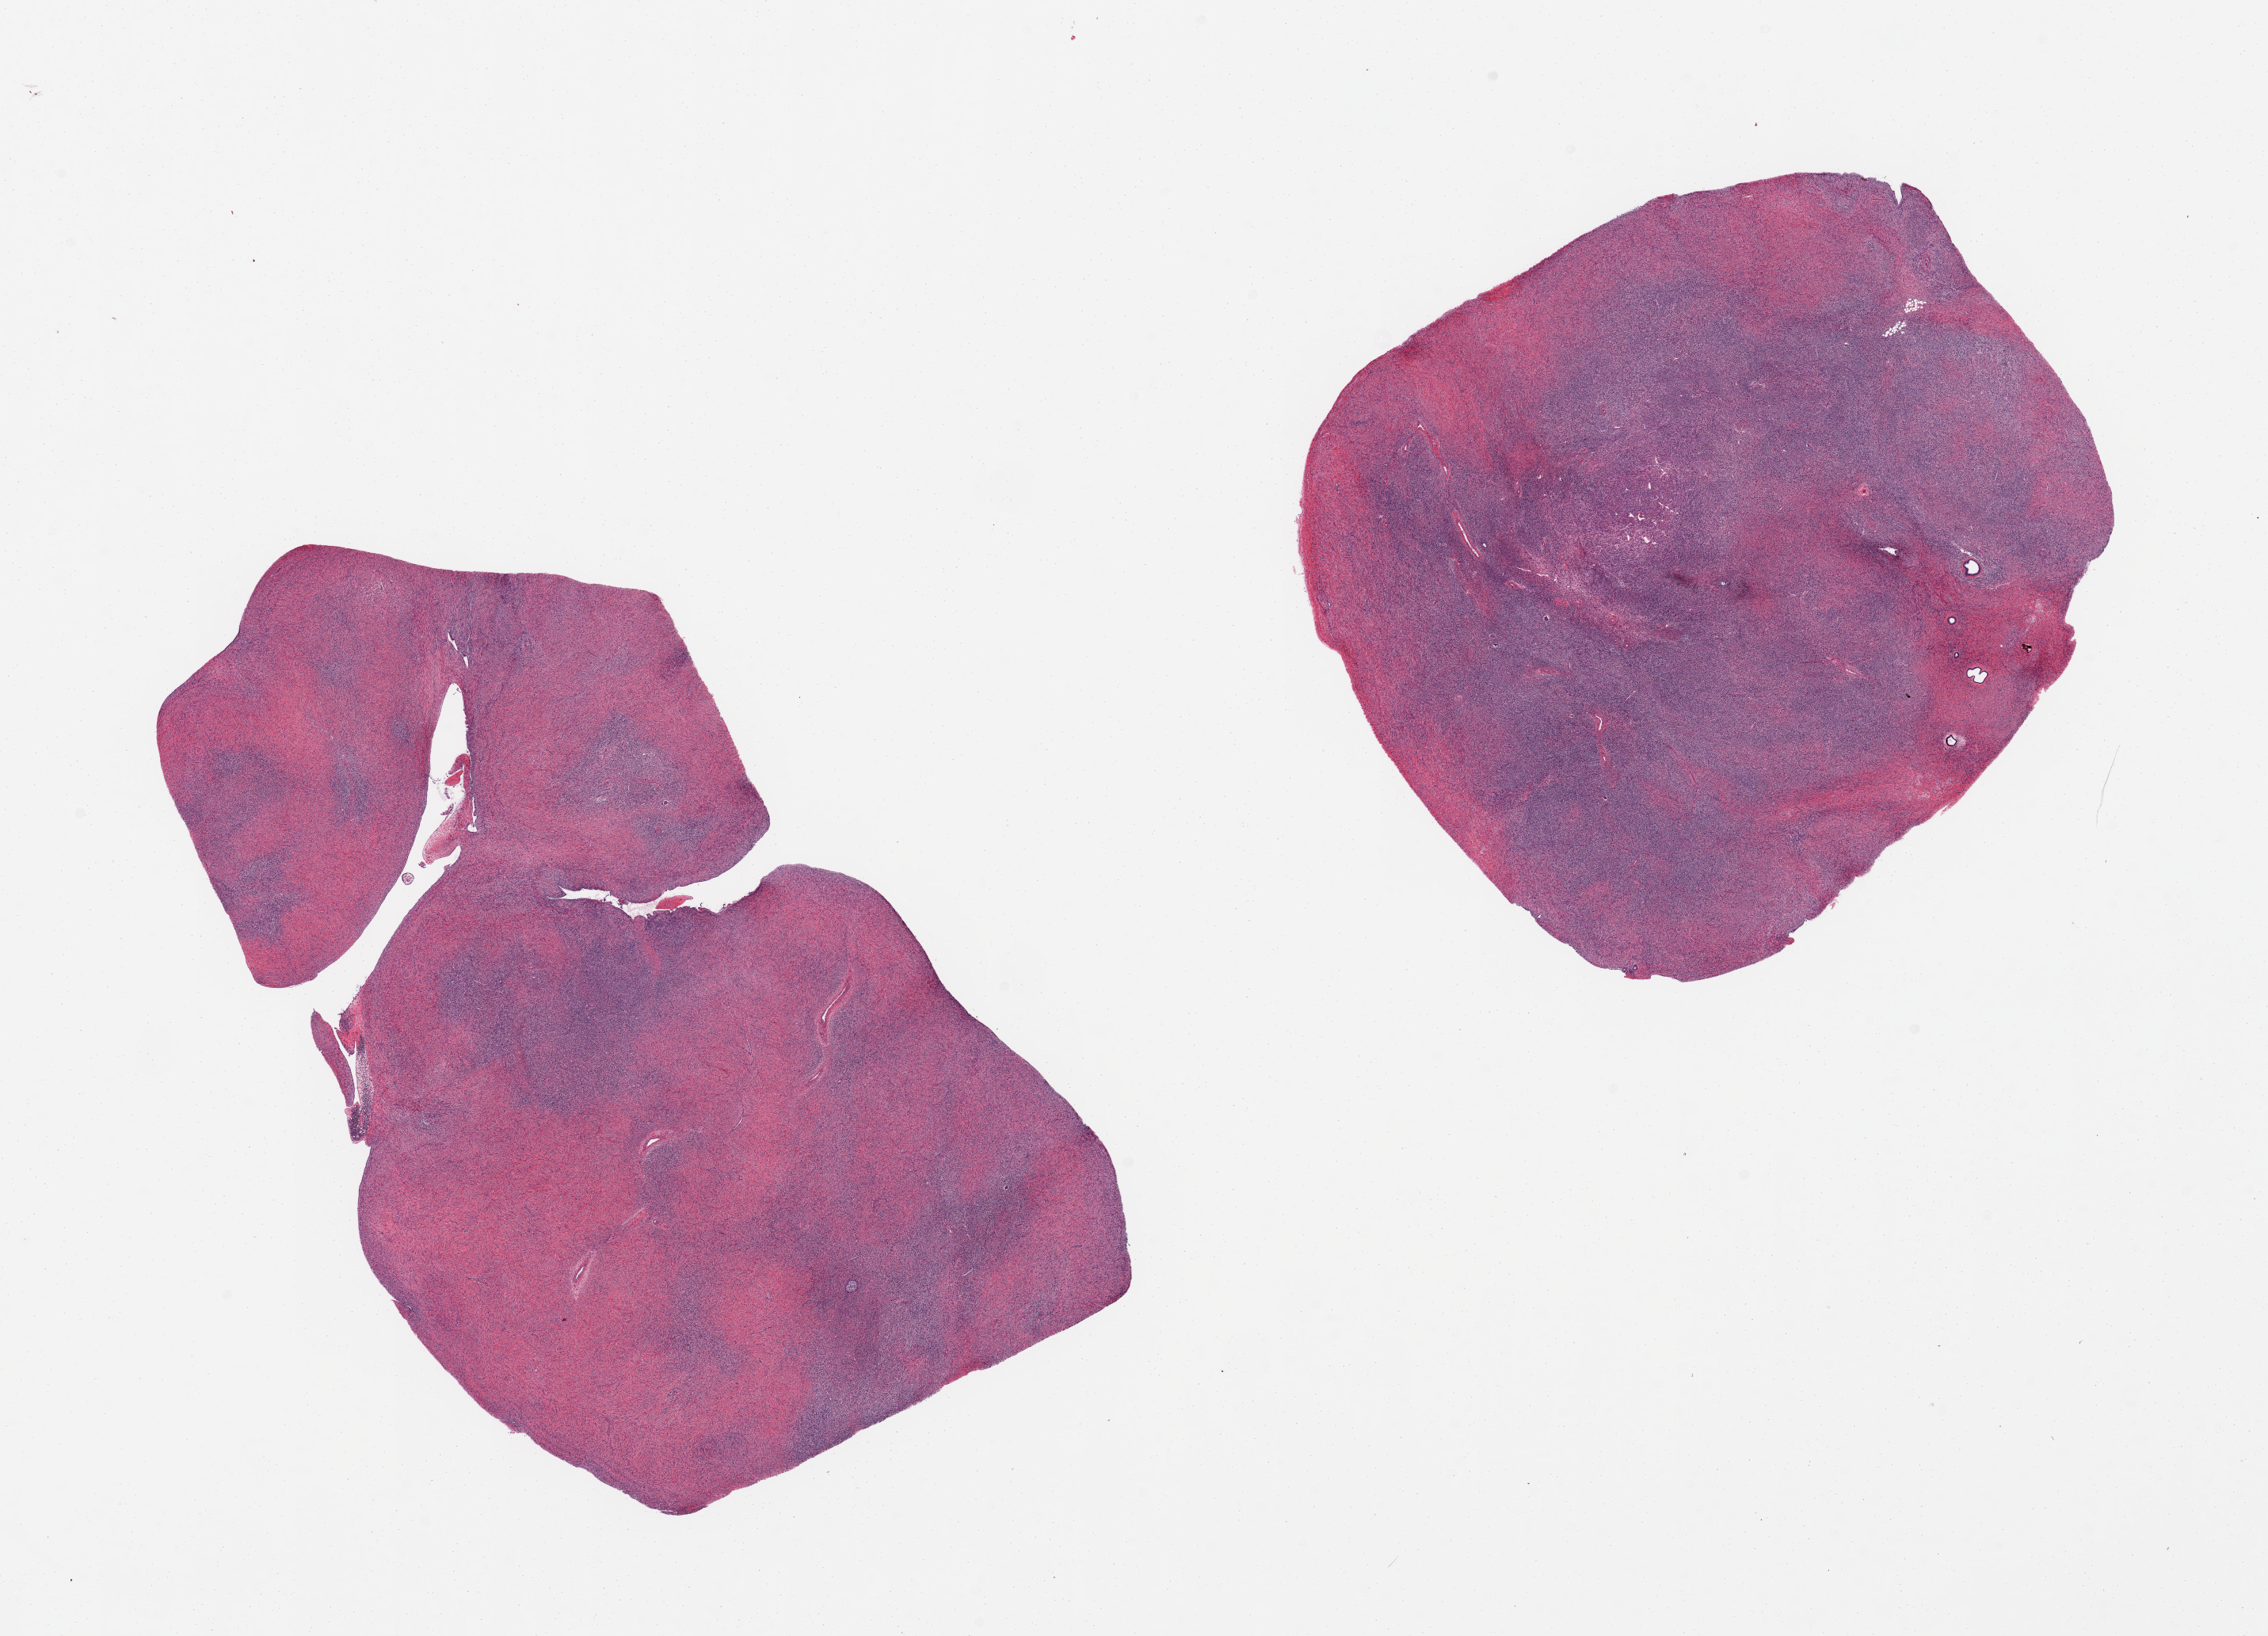
H&E whole-slide image — low-resolution overview of the scanned area, about 22.6 x 16.3 mm (slide scanned at 20x), PAXgene-fixed paraffin-embedded (PFPE) section, target tissue: ovary, tissue donor sample. Female donor.
Reviewer comment on this tissue sample: 2 pieces, few epithelial inclusion glands and rare follicle.